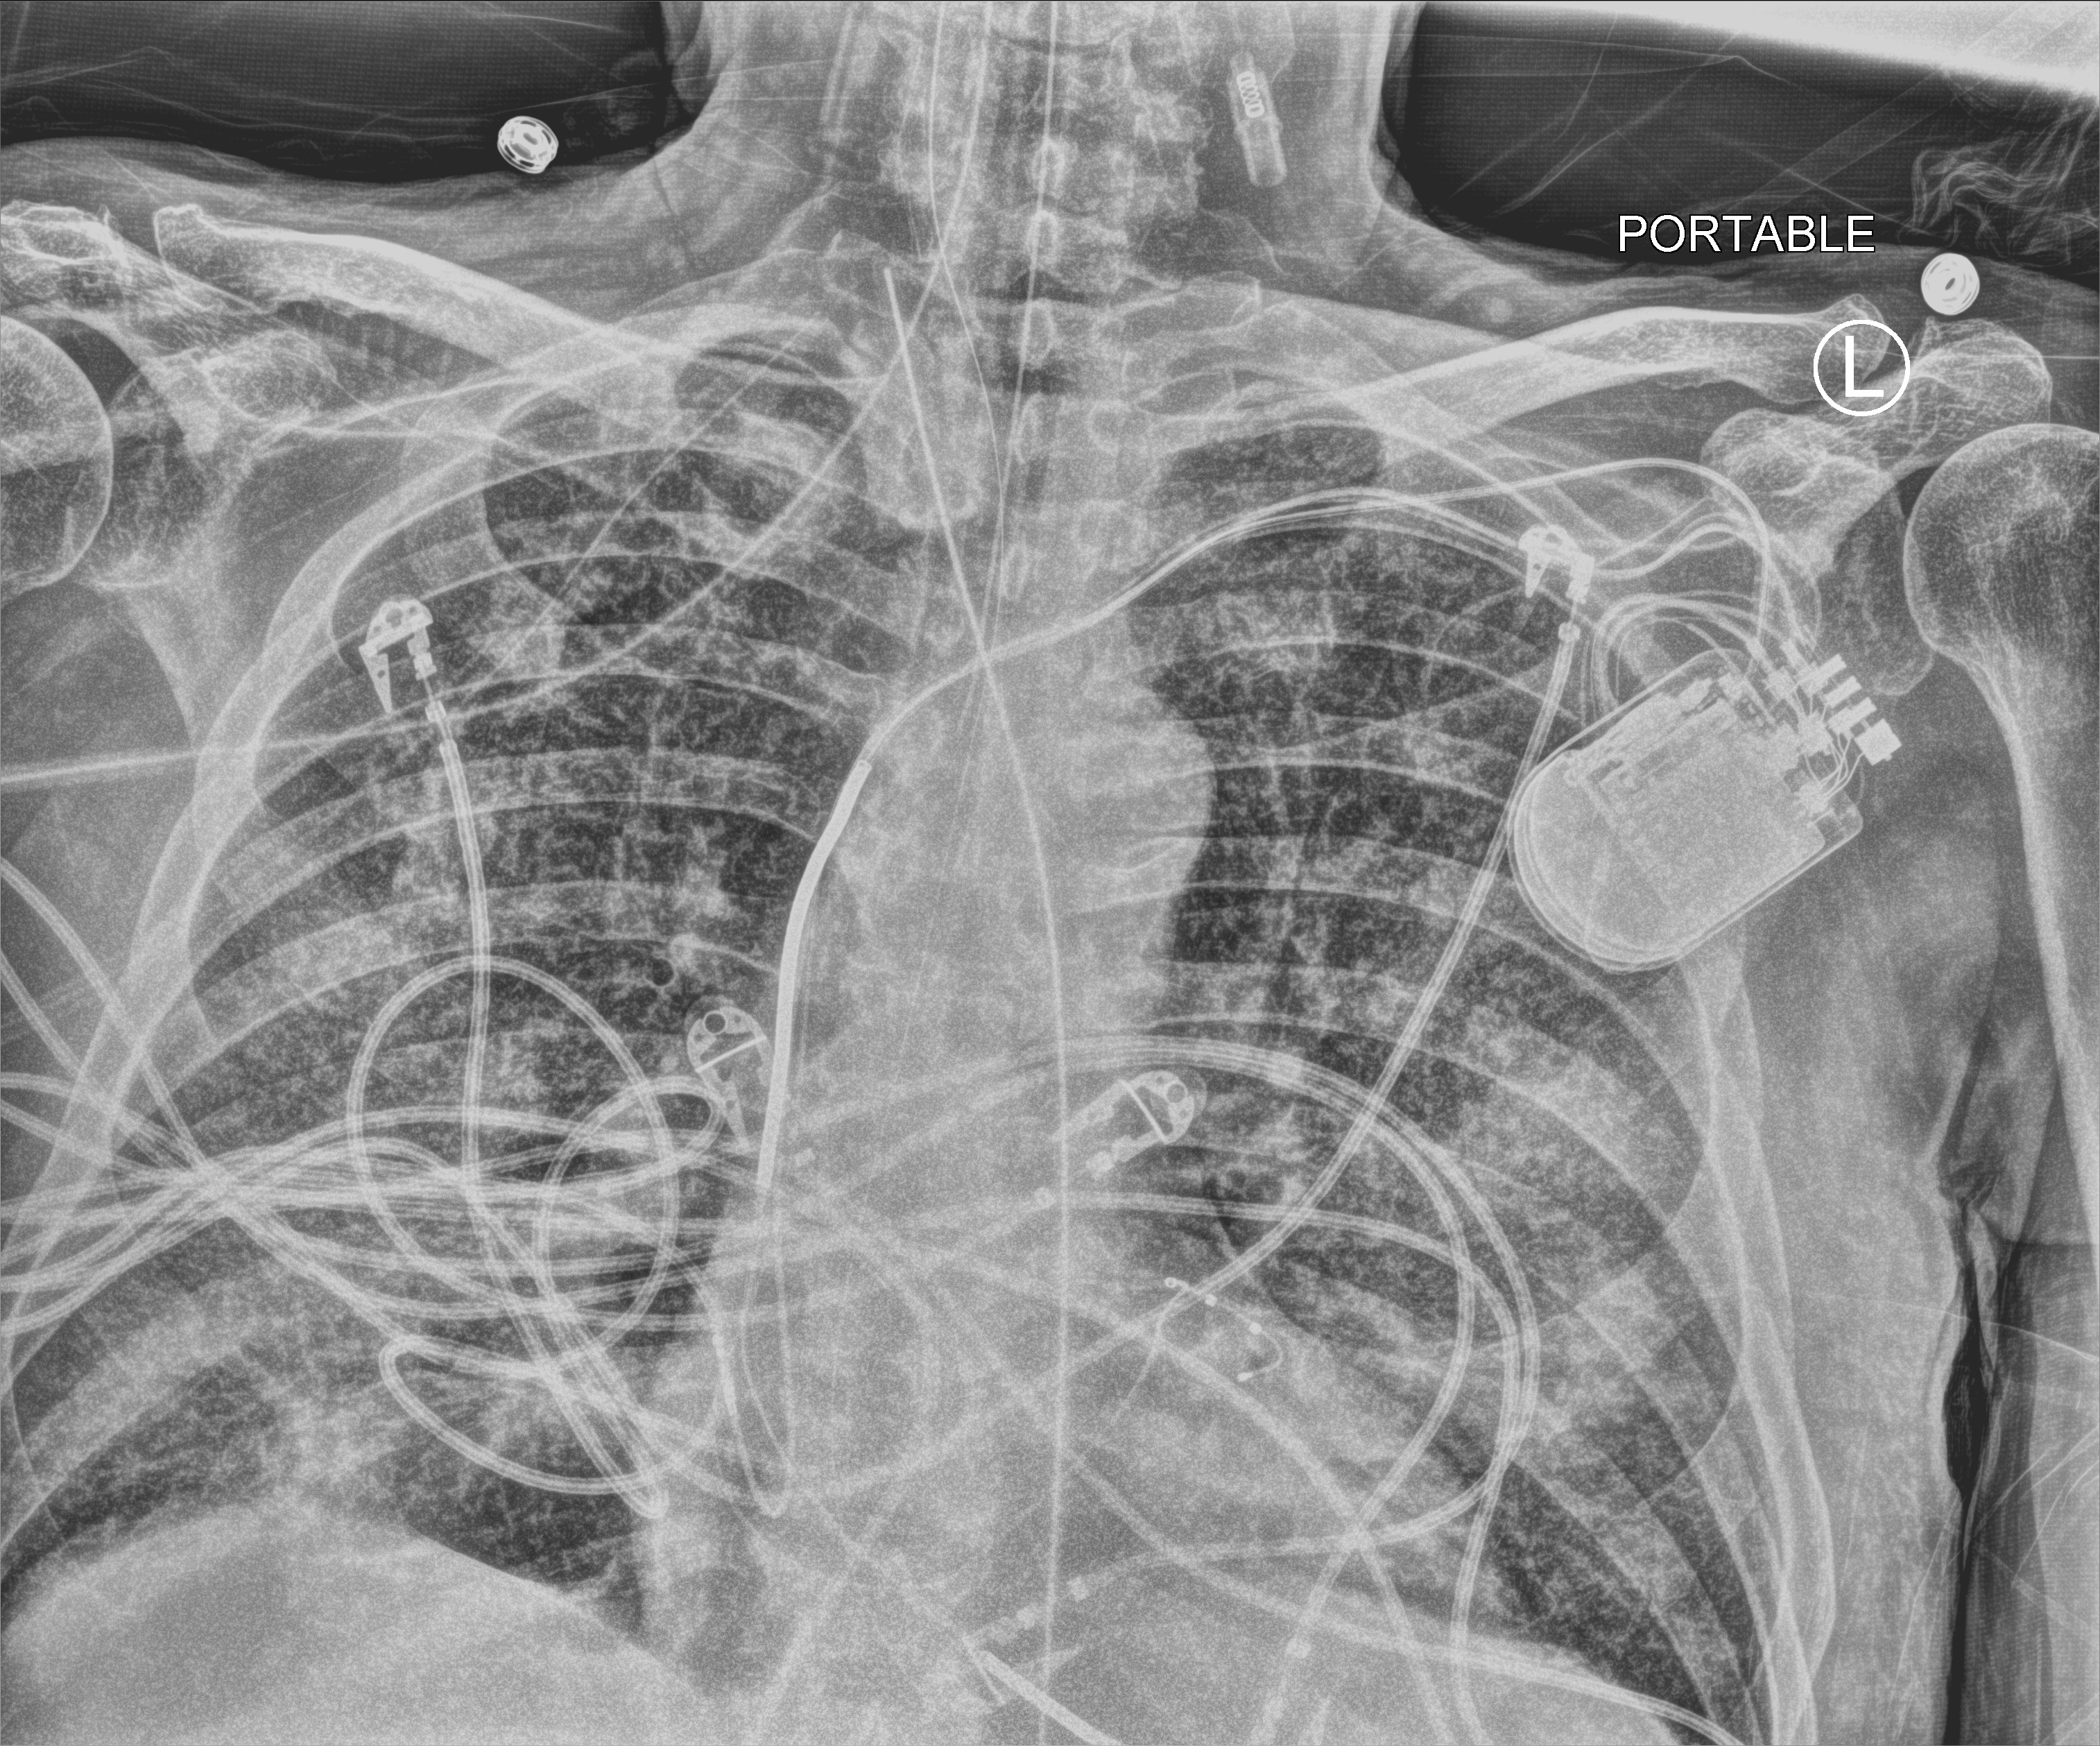
Chest X-ray (portable); anteroposterior (AP) projection. Male patient hospitalised with COVID-19, age 60–74 years.
From the hospital-stay record, not from the radiograph (when in the stay this image was taken is not recorded): admitted to intensive care during this hospital stay: yes.